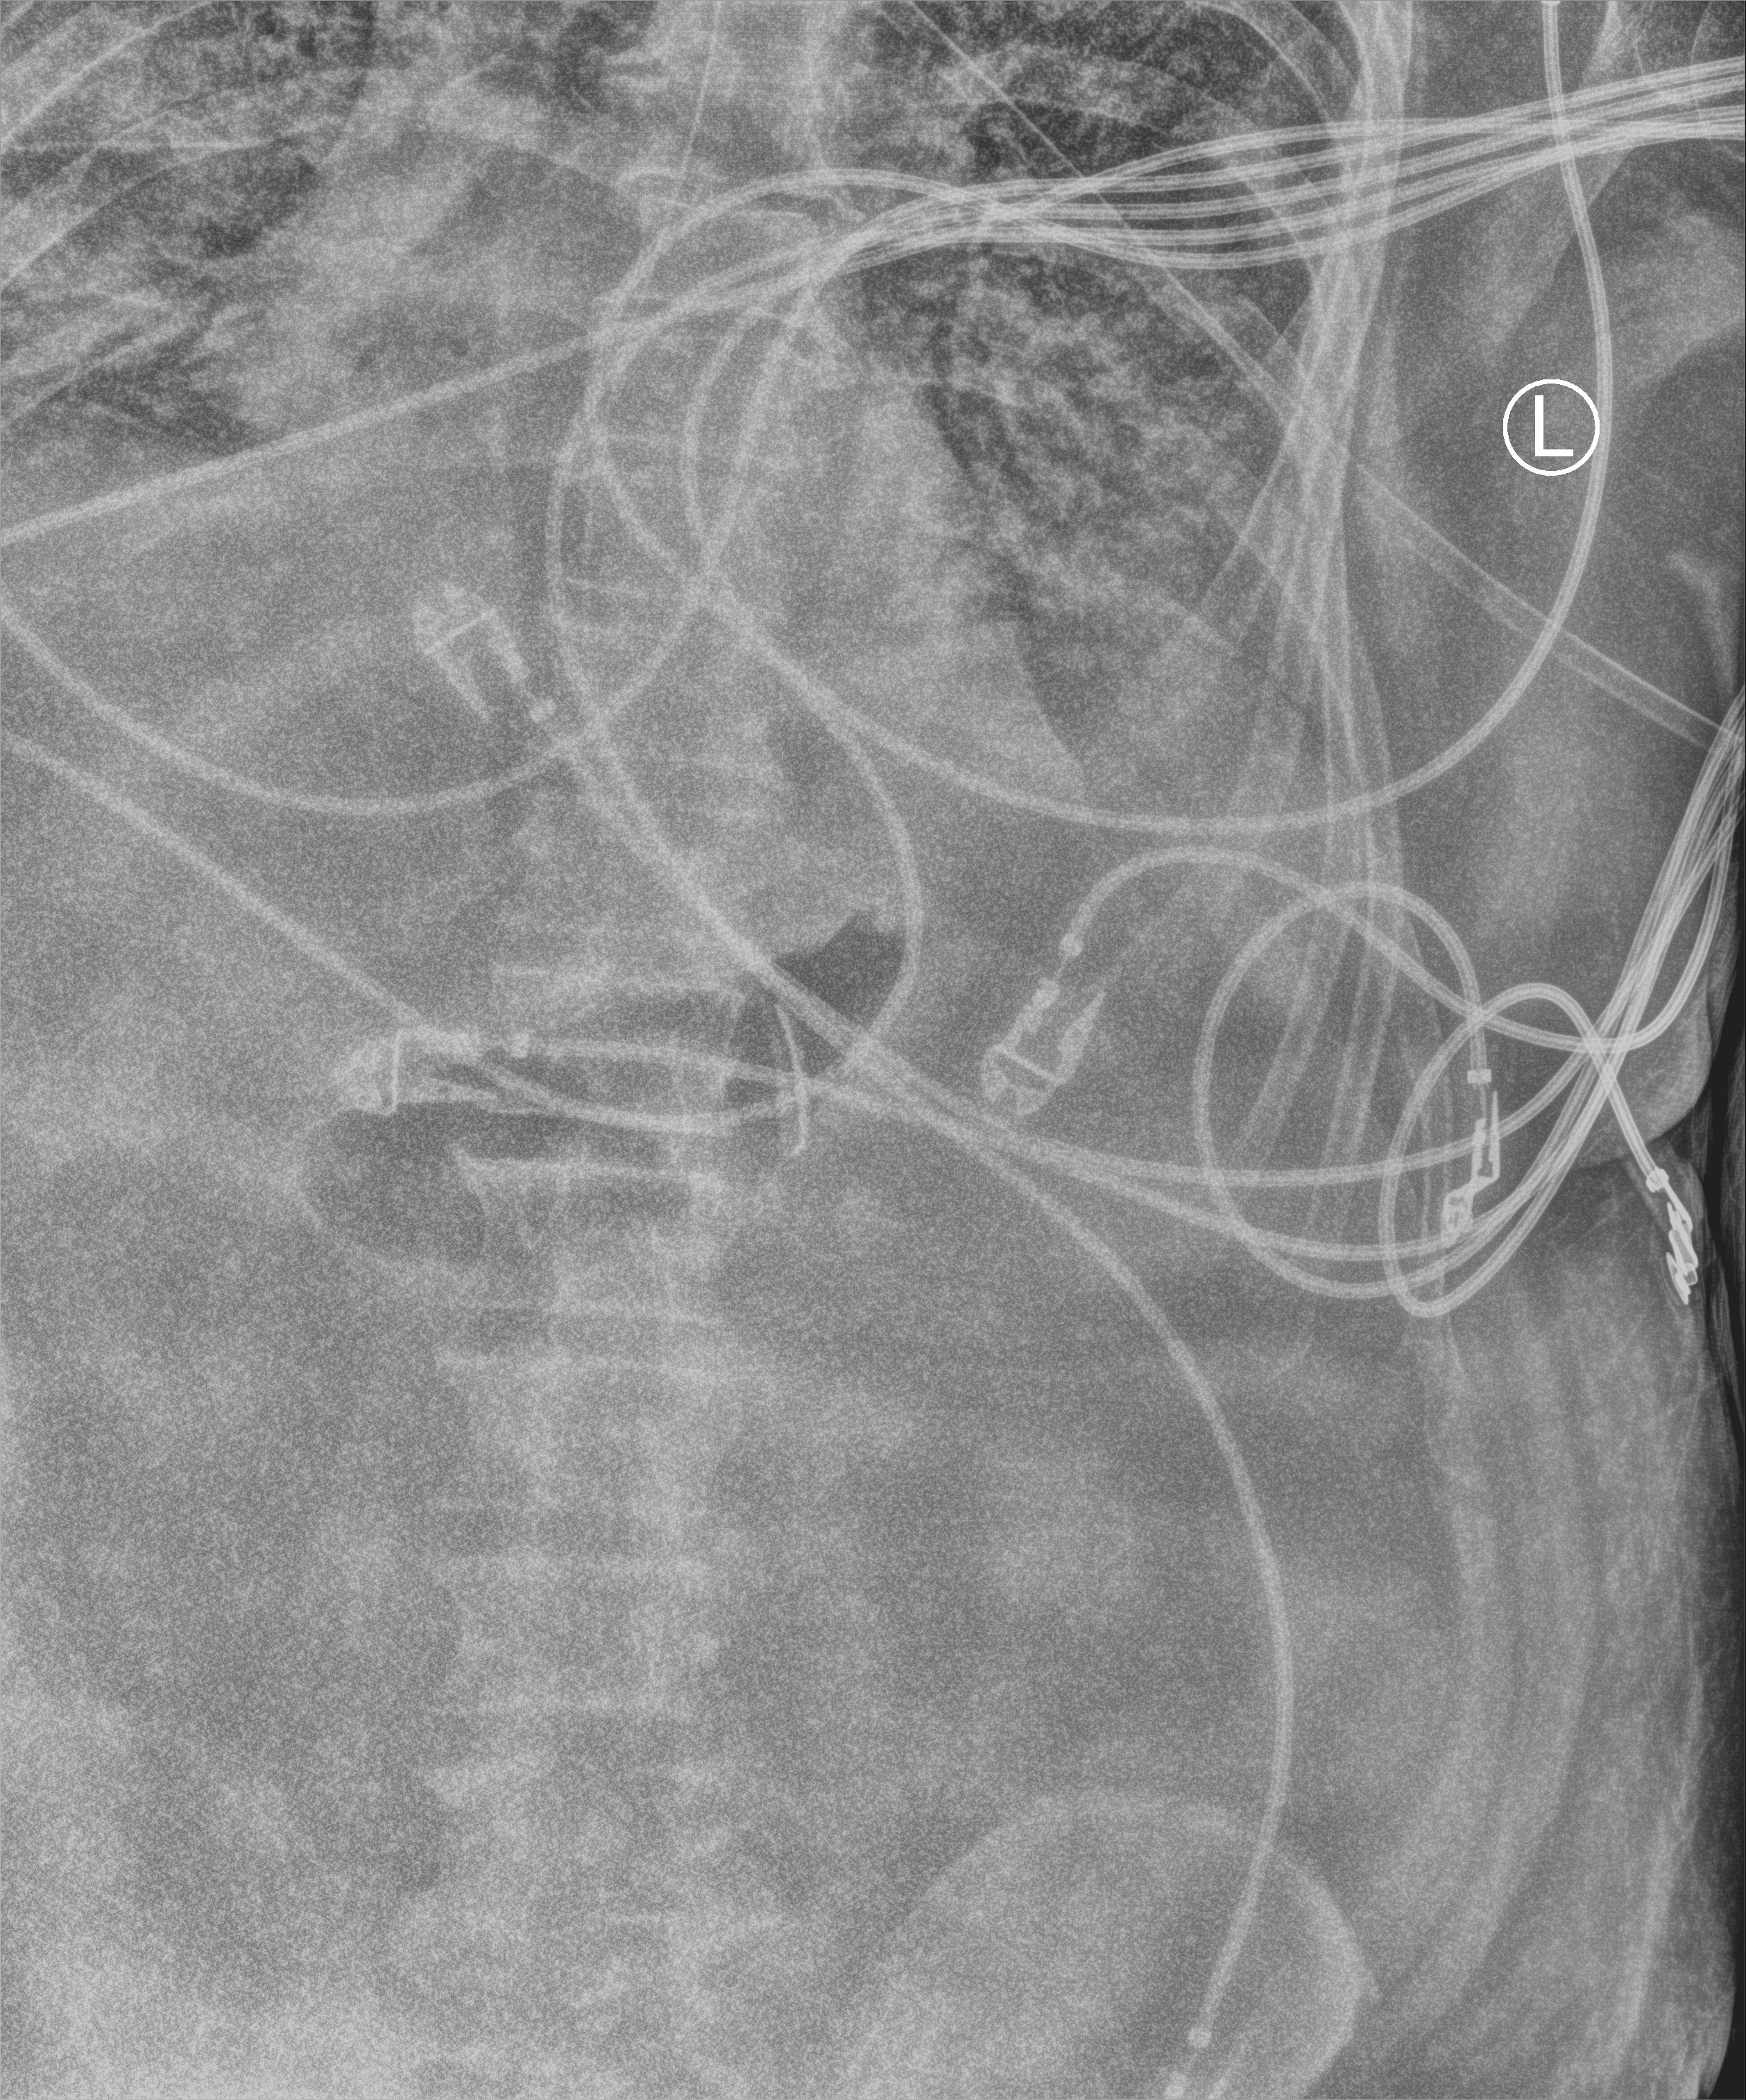
Bedside chest radiograph (computed radiography), anteroposterior (AP) projection. Male patient hospitalised with COVID-19, age 60–74 years.
From the hospital-stay record, not from the radiograph (when in the stay this image was taken is not recorded):
- admitted to intensive care during this hospital stay: yes